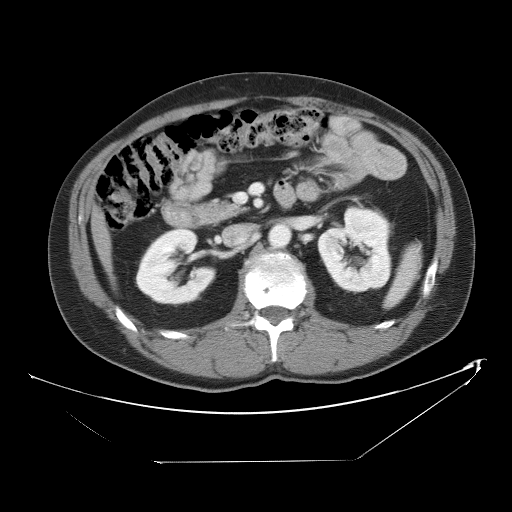
Contrast-enhanced abdominal CT, one axial slice. Reconstruction kernel STANDARD. Intravenous contrast given. Soft-tissue window (W 400 / L 40 HU). 5 mm slice thickness. 512 × 512 image matrix, field of view 438 × 438 mm. Male patient, age 59 years. From the clinical record (not read from this slice): diagnosis: colorectal cancer liver metastases, imaged before liver resection; multiple liver metastases: yes; largest metastasis: 8.5 cm; disease in both lobes: no.
Outlined on this slice (outlined manually by an expert reader):
- liver: box from (x=94, y=214) to (x=111, y=265) px
- planned liver remnant (the part of the liver to remain after resection): (x=94, y=215)–(x=111, y=265)